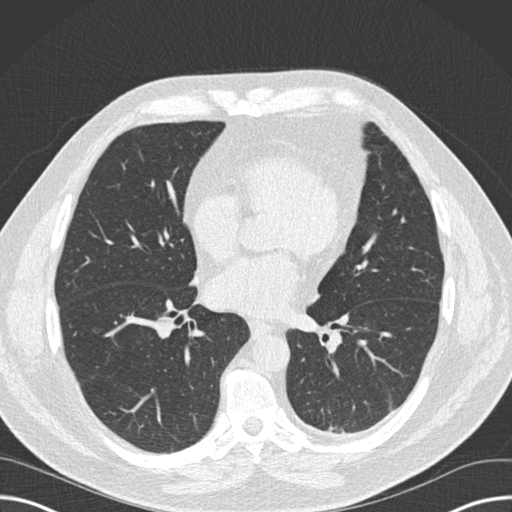
Low-dose screening chest CT, one axial slice. Slice 73 of 160 in the series (ordered by position). 120 kVp. Lung window (W 1500 / L -600 HU). 2 mm slice thickness. 512 × 512 image matrix, field of view 382 × 382 mm.
Structures marked on this image (expert manual segmentation):
- lesion 1 (tumor, upper lobe of left lung): bounding box <340,432,346,436> (left, top, right, bottom; pixels)